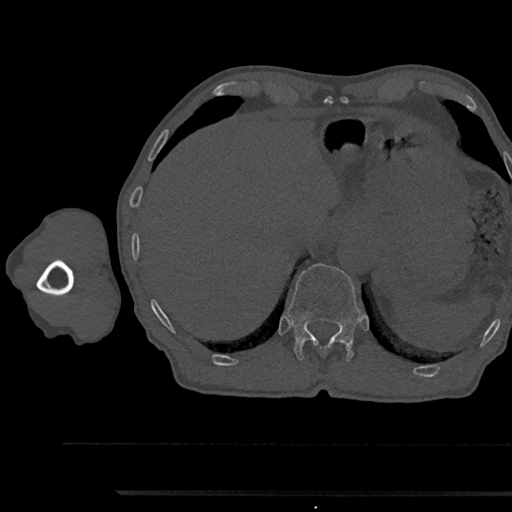
CT including the spine, one axial slice; slice 737 of 797 in the series (ordered by position); 120 kVp; bone window (W 1800 / L 400 HU); 512 × 512 image matrix, field of view 367 × 367 mm. Patient: male, 79 years. Case-level facts recorded for this patient, not image findings: primary cancer: prostate.
Annotated regions visible in this slice (semi-automatically segmented with operator editing):
- T12 vertebra: bounding box [x1, y1, x2, y2] px = [287, 263, 360, 362]